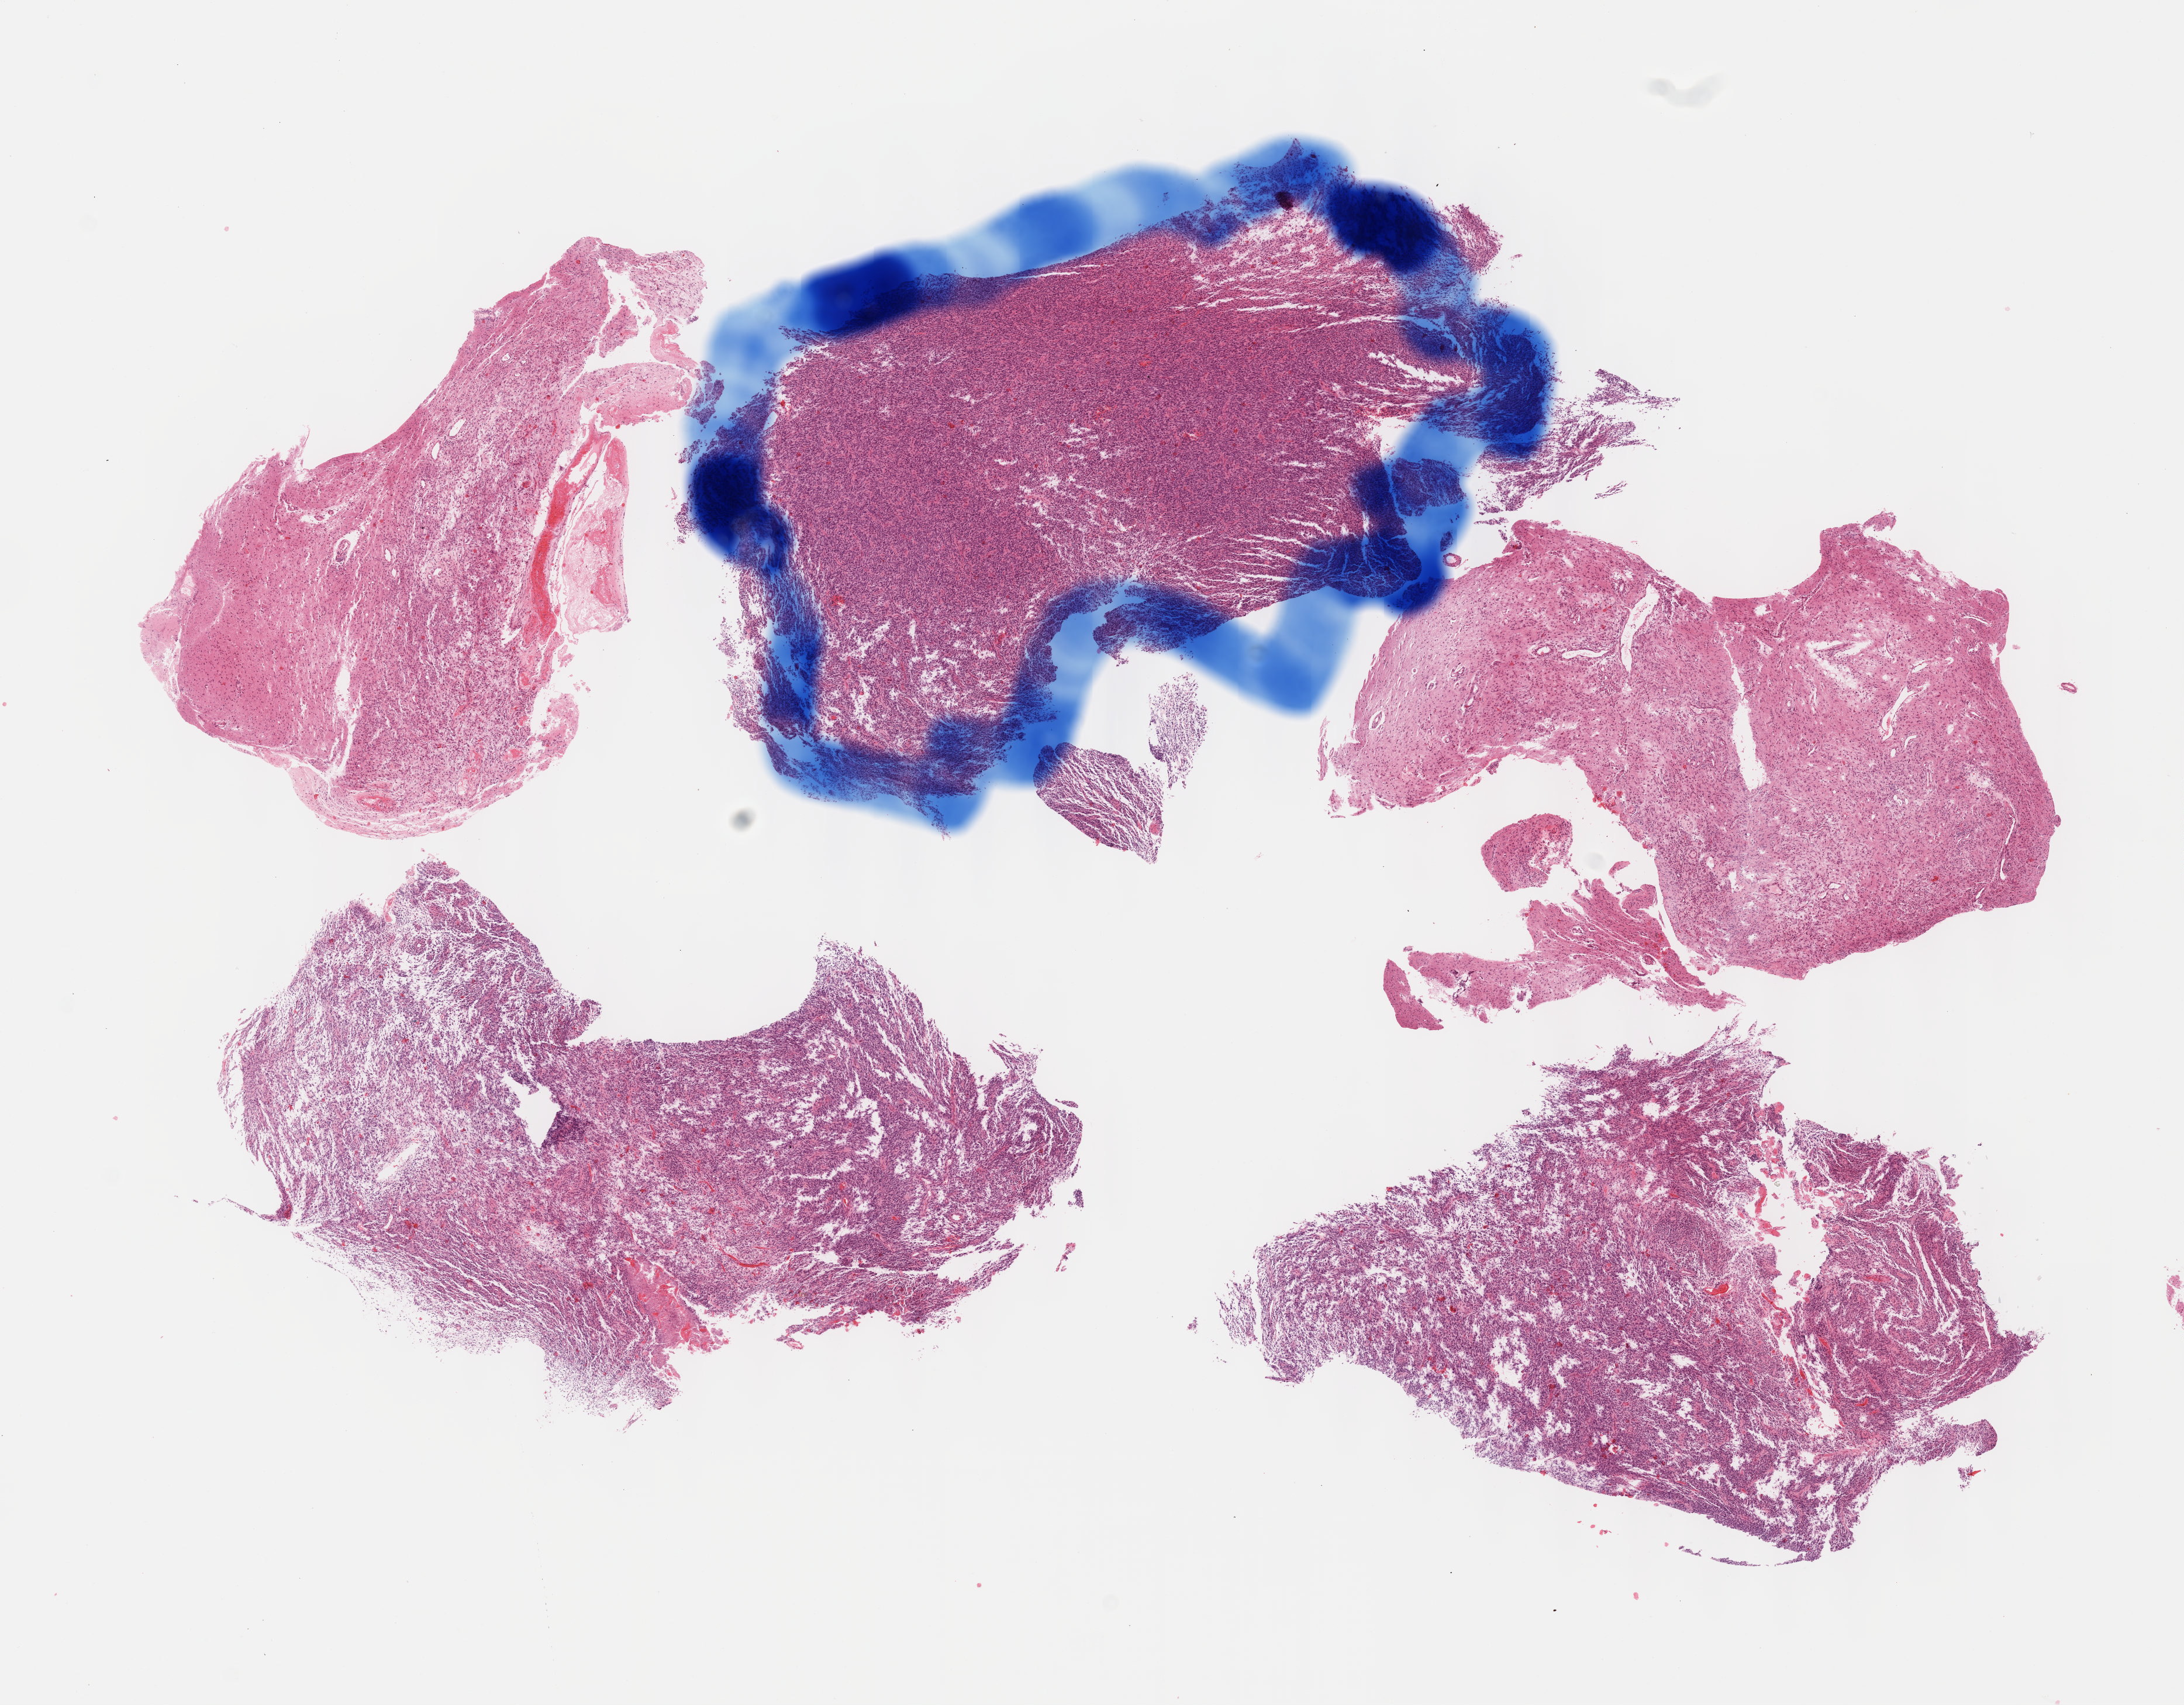
H&E-stained whole-slide image, low-resolution overview of the scanned area, about 15.1 x 11.8 mm (acquisition: 40x scan), FFPE section, primary tumour sample from the brain. Patient: female, age at initial diagnosis 51 years.
Pathologic diagnosis: Glioblastoma.